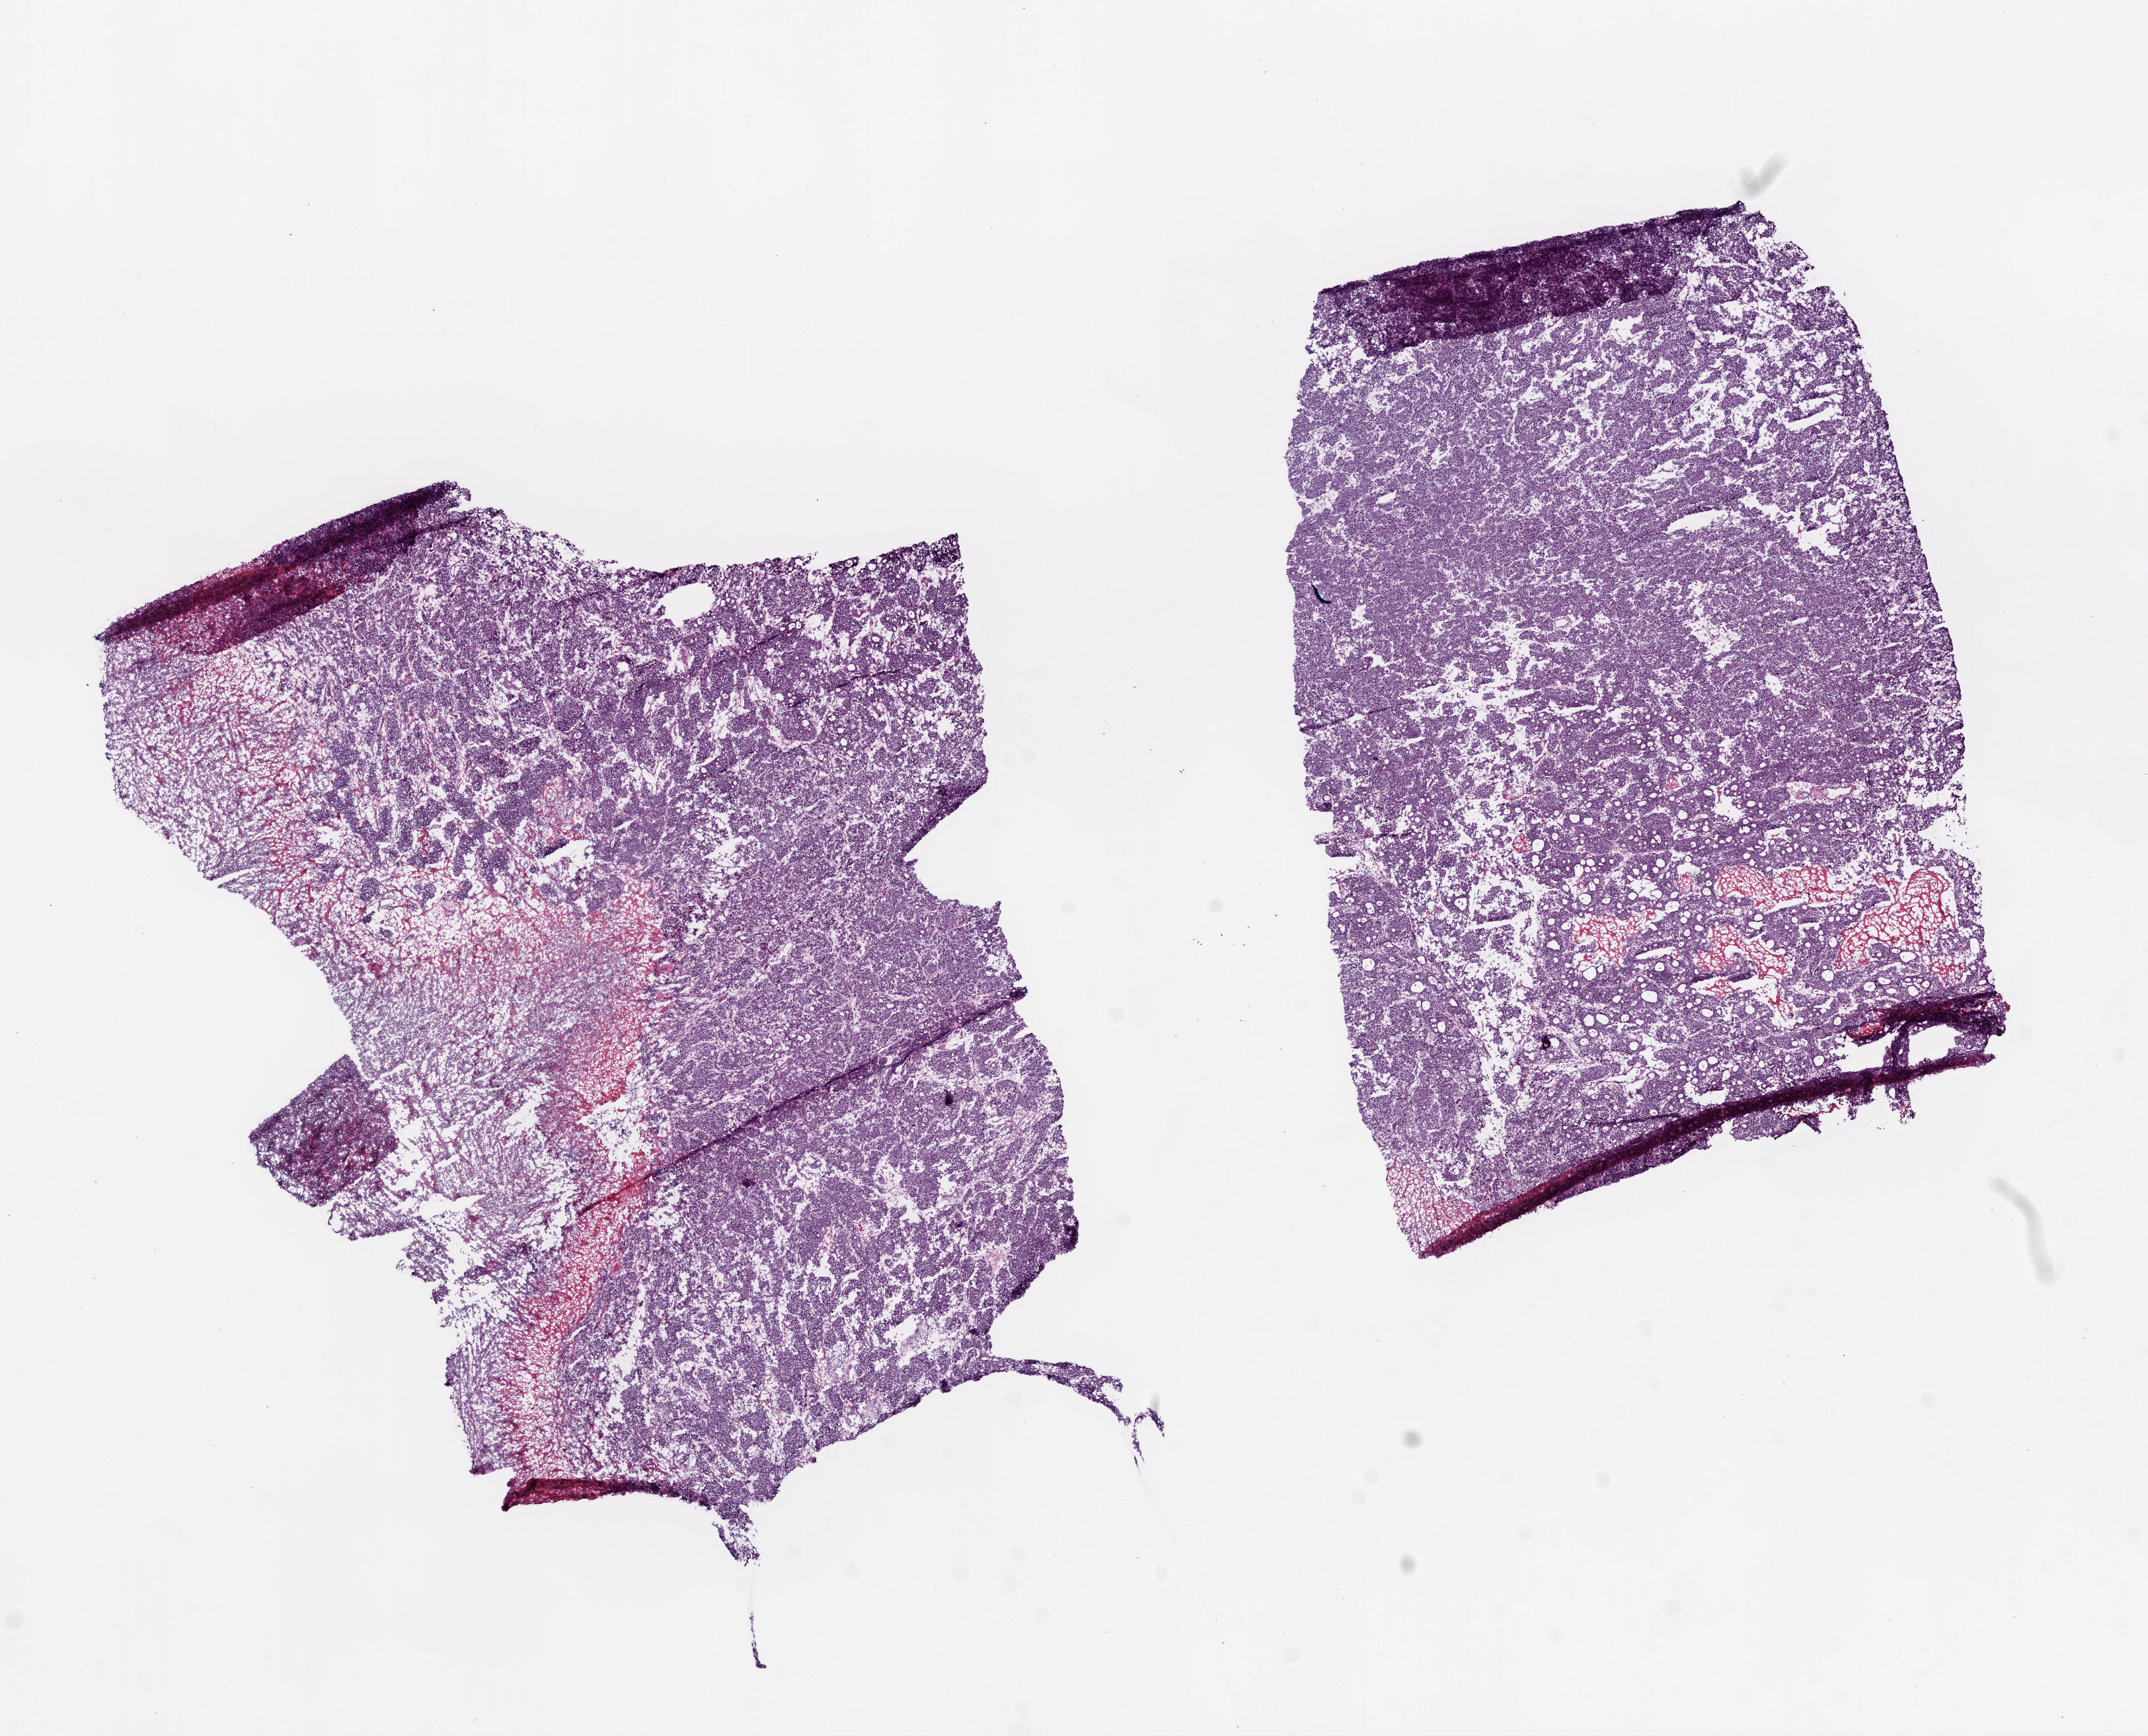
Whole-slide histology image, H&E — whole scanned area (about 13.0 x 10.5 mm, slide scanned at 20x) shown as a low-resolution overview, frozen section from the top of the tissue portion, sample: primary tumour, stomach. Male, age 70 years at initial diagnosis. Histologic grade: G3 (poorly differentiated). Pathologist review of this section (percent, as recorded): tumour cells 85%, tumour nuclei 75%, normal cells 0%, stromal cells 5%, necrosis 10%.
AJCC pathologic stage: IV (6th edition). Pathologic diagnosis: Adenocarcinoma, intestinal type. Lymph nodes positive (case pathology): 39 of 40 examined.